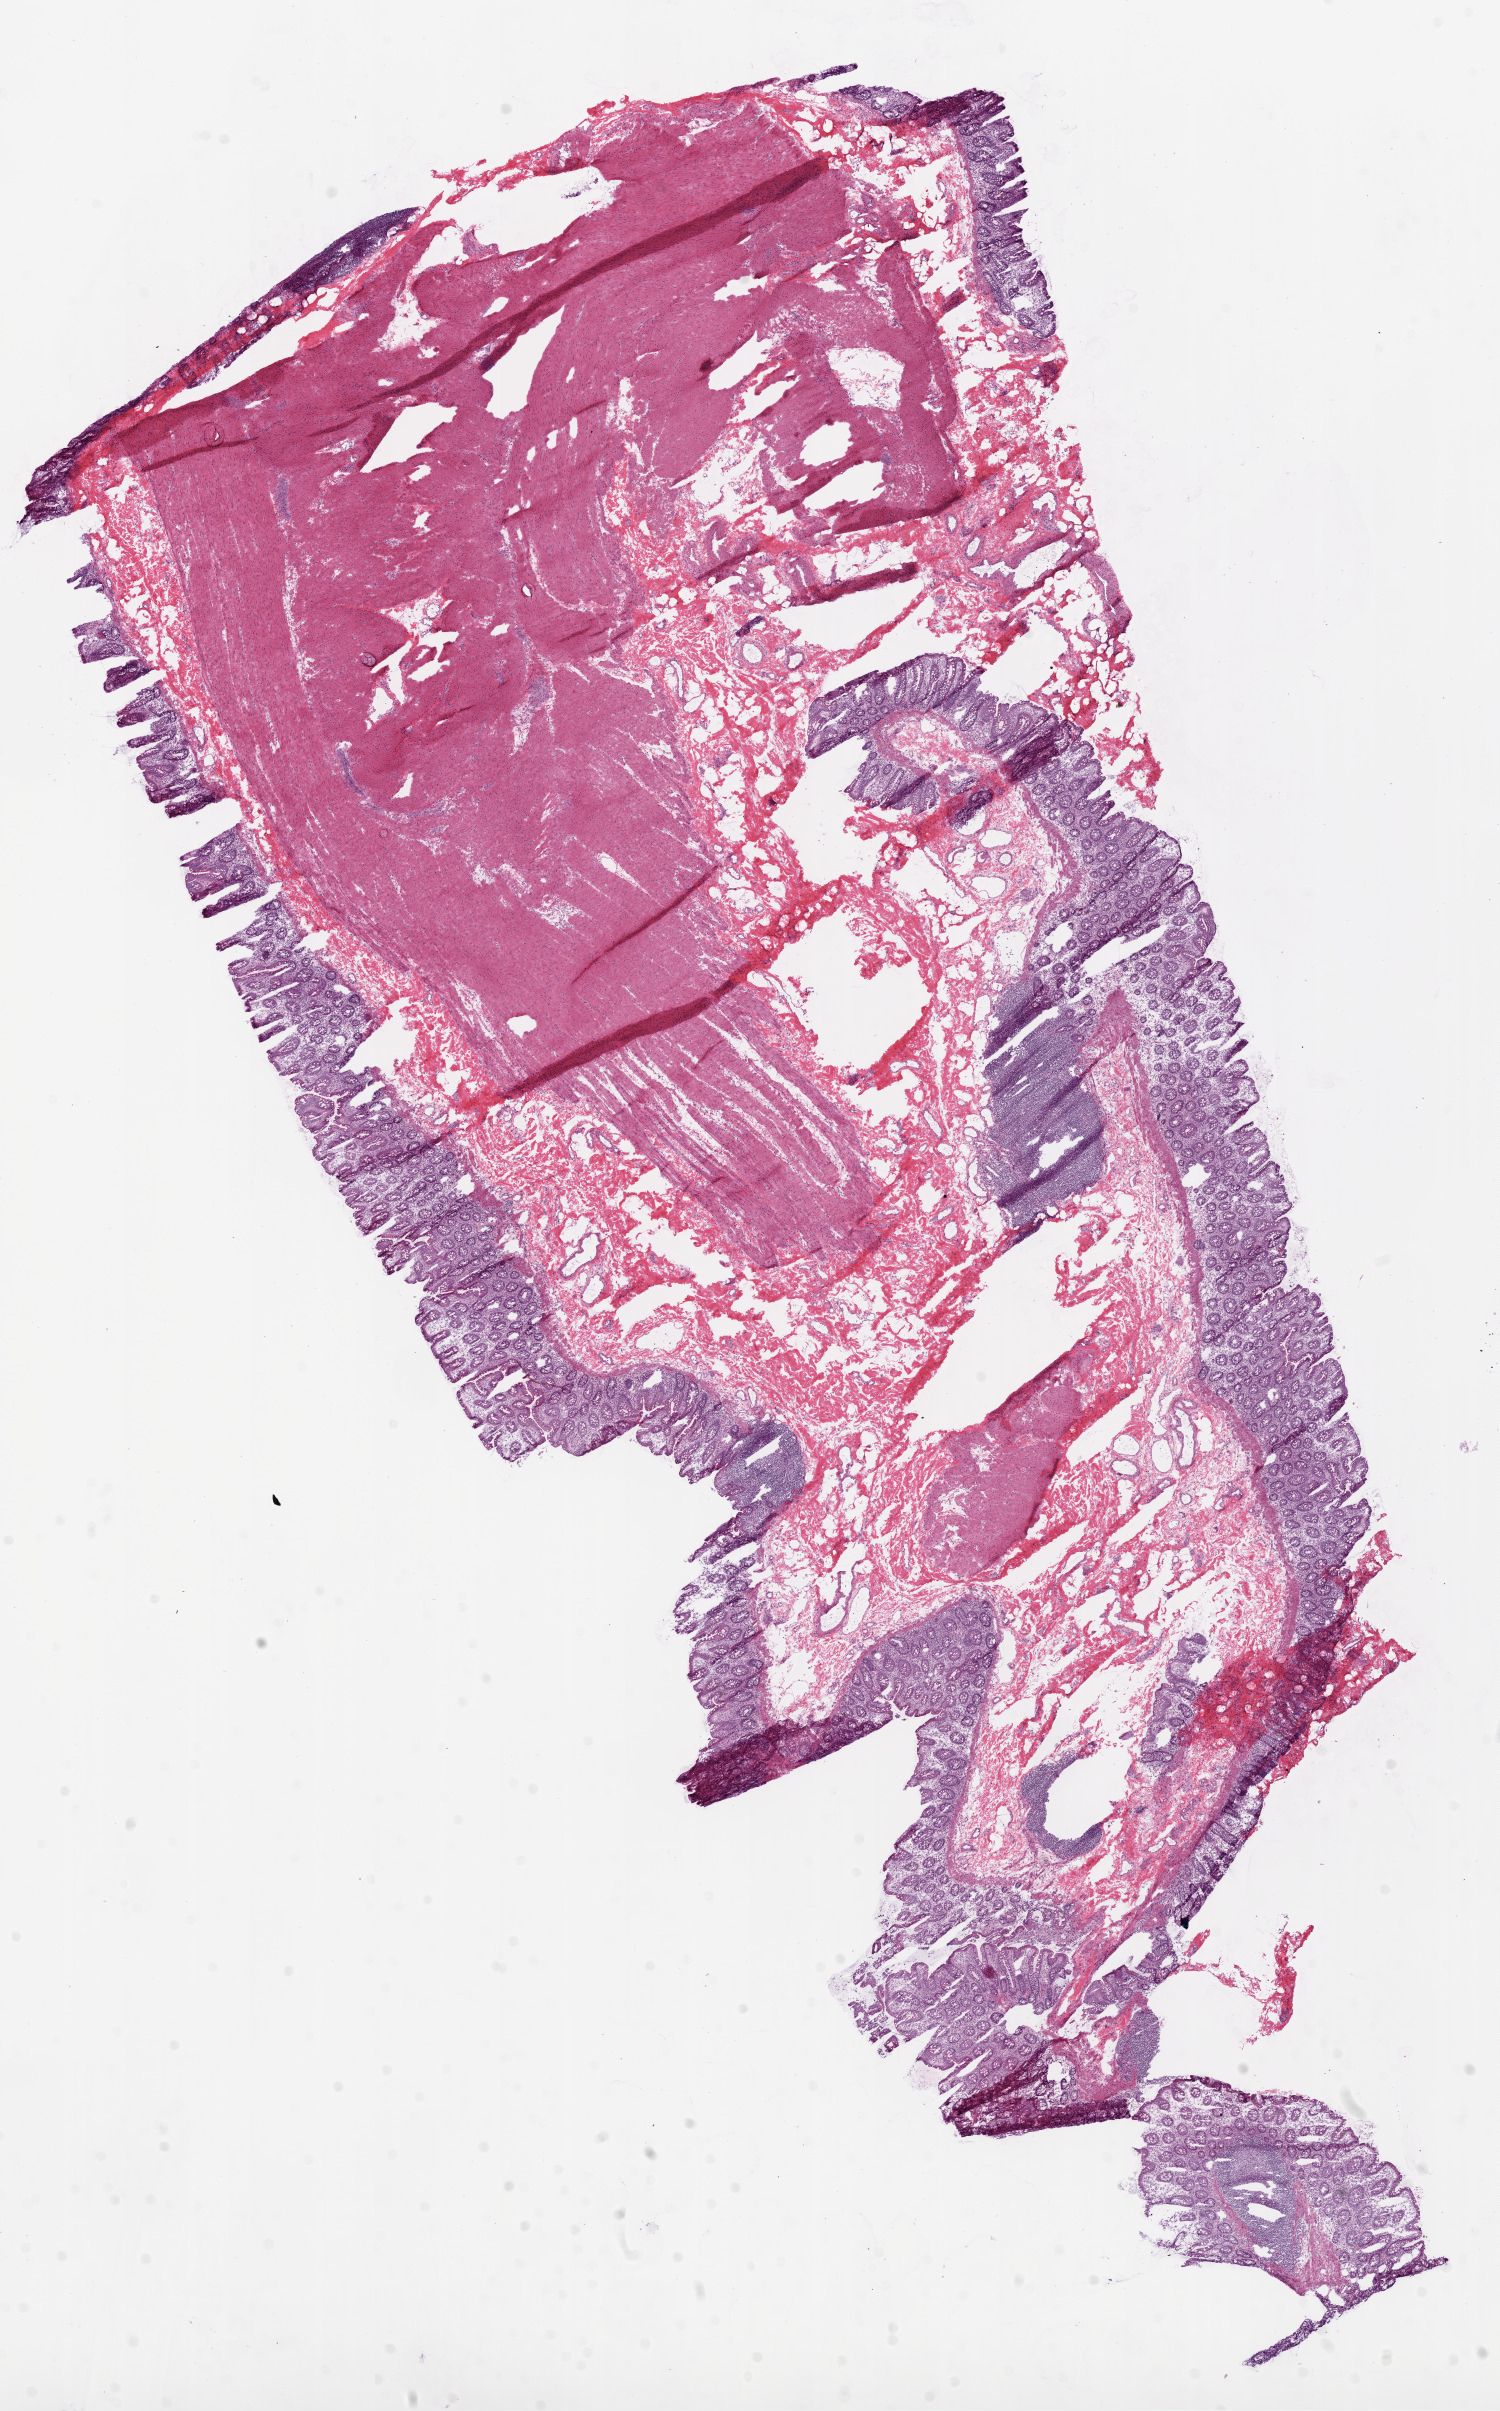
Digitized H&E tissue section (whole slide), shown as a low-resolution overview of the whole scanned area (about 12.0 x 19.3 mm, from a 20x scan), frozen section from the top of the tissue portion, colon, solid tissue normal (non-tumour tissue) sample. Female patient; age at initial diagnosis 57 years.
This section: solid tissue normal (non-tumour) sample from the same patient. Patient diagnosis: Adenocarcinoma, NOS.